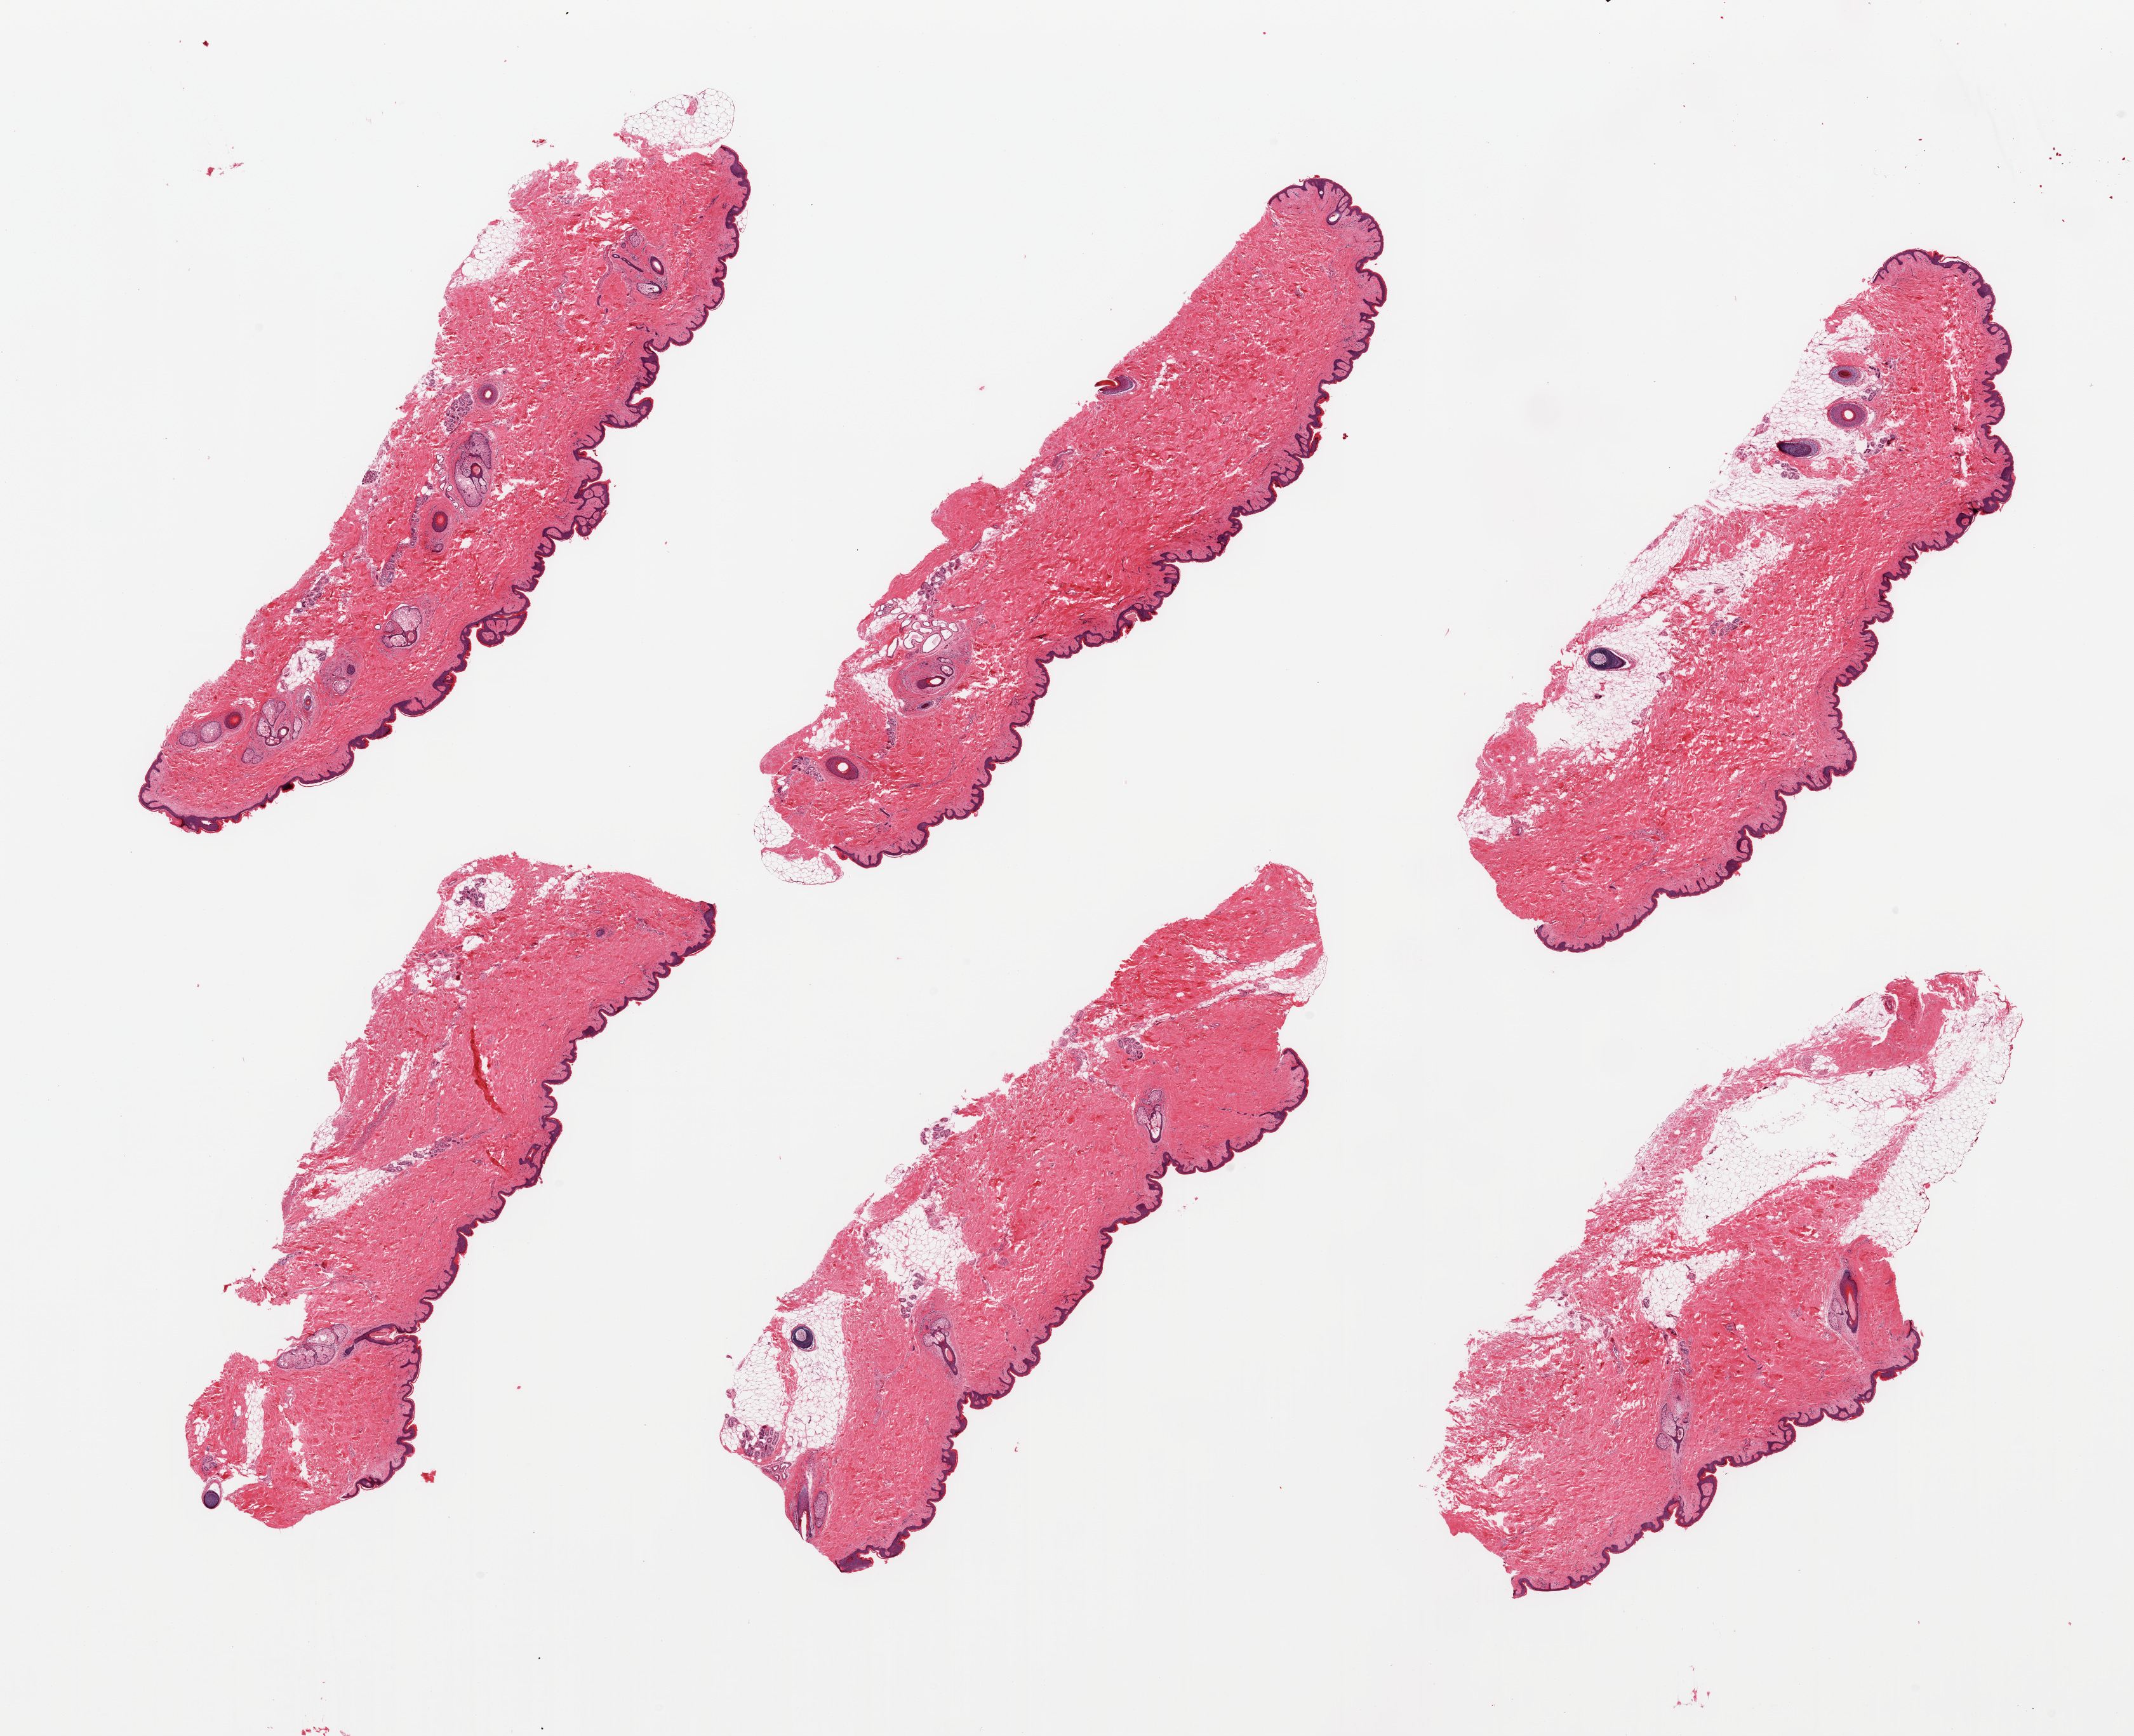
Digitized hematoxylin and eosin (H&E)-stained section, brightfield — low-resolution overview of the scanned area, about 26.6 x 21.6 mm (slide scanned at 20x), PAXgene-fixed, paraffin-embedded tissue, target tissue: skin of suprapubic region, tissue donor sample.
- pathologist's review note for this sample: 6 pieces; include 5-15% attached and internal fat, small amount of carryover